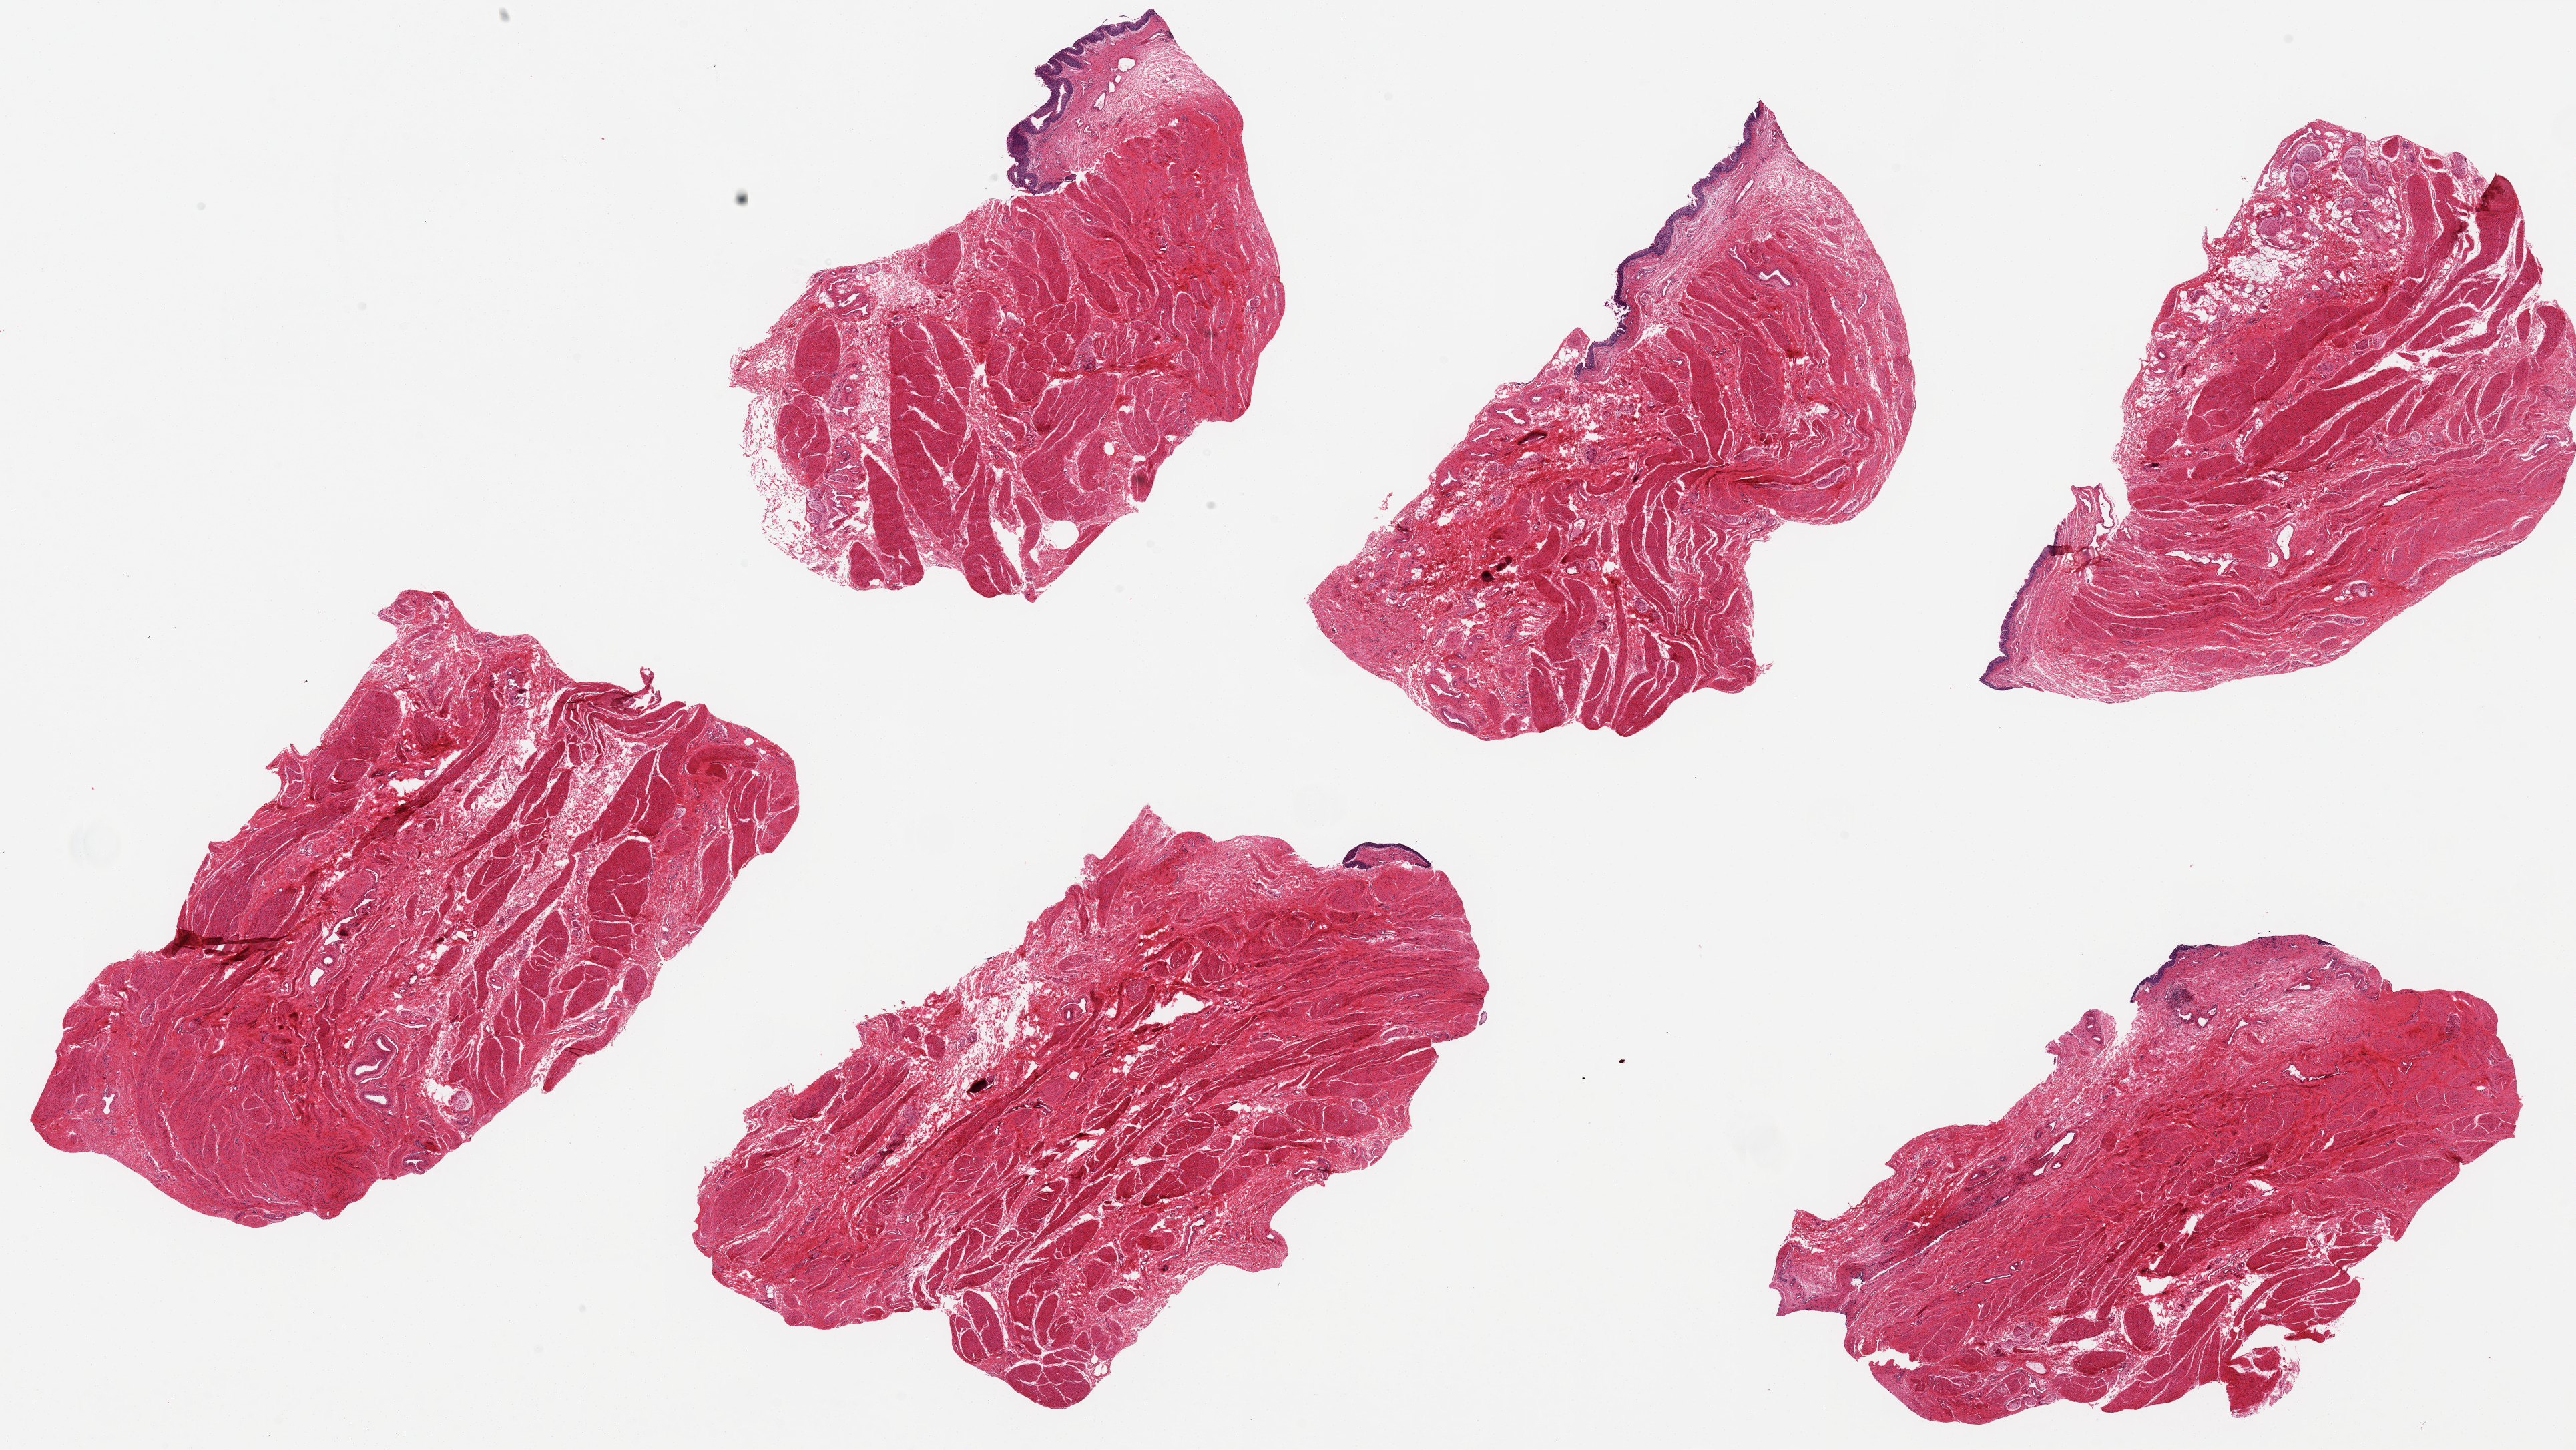
Whole-slide image, hematoxylin and eosin (H&E) stain, brightfield, low-resolution overview of the scanned area, about 30.5 x 17.2 mm; PAXgene-fixed, paraffin-embedded tissue; sampled site (target tissue): urinary bladder; tissue donor sample. Donor: female.
• review note (as recorded): 6 pieces up to 8x5 mm; surface focally present in 5 of 6 pieces (maximum length 3.7 mm)